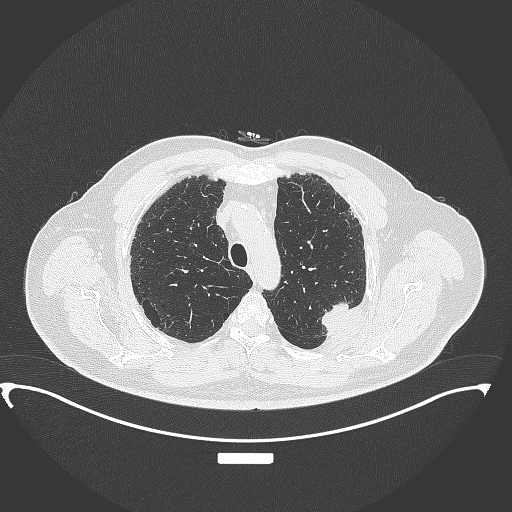
Chest CT, one axial slice; position 281 of 350 along the scan axis; reconstruction kernel B70f; 120 kVp; lung window (W 1500 / L -600 HU); 1 mm slice thickness; 512 × 512 image matrix. Male patient, age 64 years. From the clinical record (not read from this slice): clinical TNM (as recorded): T1c N1 M1.
Annotated regions visible in this slice (rectangle marked by the reading radiologist):
- lung tumour (recorded histology: adenocarcinoma): bounding box (x1, y1, x2, y2) in pixels: (316, 294, 362, 347)